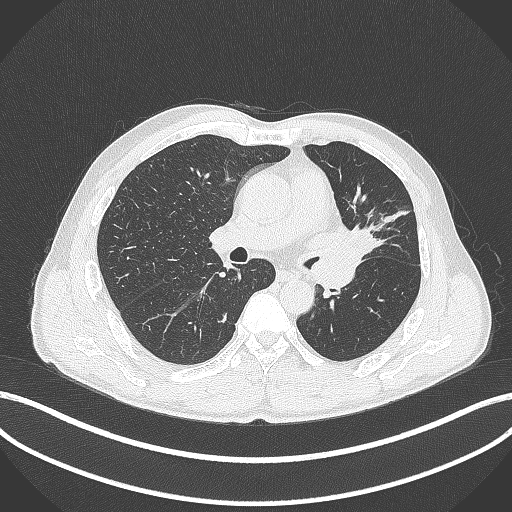
Chest CT, one axial slice. Position 241 of 429 along the scan axis. Reconstruction kernel B70f. 120 kVp. Lung window (W 1500 / L -600 HU). 512 × 512 image matrix. Male patient, age 57 years. From the clinical record (not read from this slice): clinical TNM (as recorded): T2b N0 M0.
Outlined on this slice (rectangle marked by the reading radiologist):
- lung tumour (recorded histology: squamous cell carcinoma): bounding box [x1, y1, x2, y2] px = [318, 216, 385, 264]